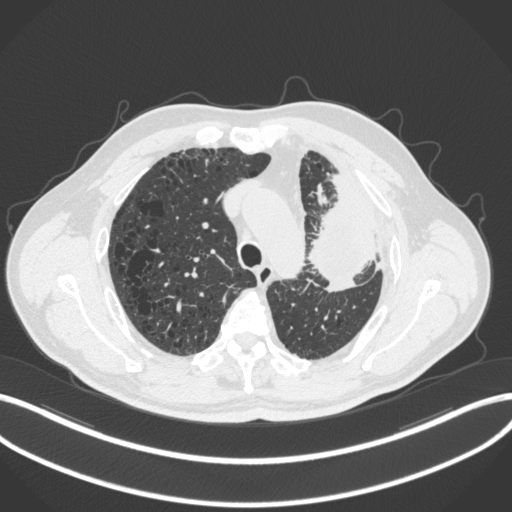
Chest CT, one axial slice; reconstruction kernel B31f; lung window (W 1500 / L -600 HU); 1 mm slice thickness; 512 × 512 image matrix. Male patient, age 68 years. From the clinical record (not read from this slice): clinical TNM (as recorded): T3 N3 M1.
Annotated regions visible in this slice (bounding box drawn by a radiologist):
- lung tumour (recorded histology: adenocarcinoma): box from (x=306, y=178) to (x=380, y=294) px